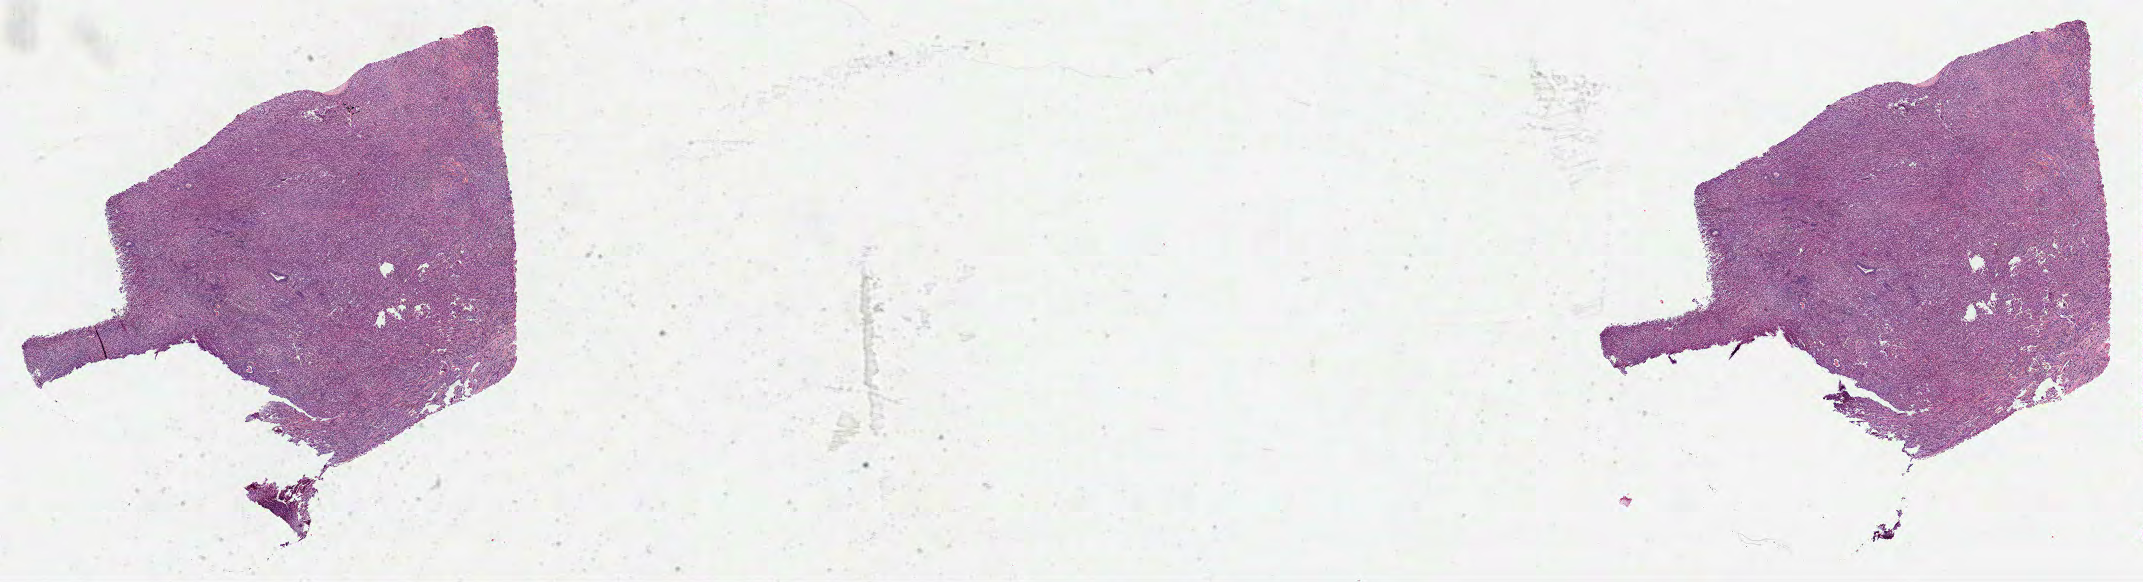
H&E whole-slide image, whole scanned area (about 34.6 x 9.4 mm, acquisition: 40x scan) shown as a low-resolution overview, formalin-fixed paraffin-embedded (FFPE) diagnostic section, sample: primary tumour, lung. Female patient; age at initial diagnosis 50 years.
TNM: T2 N1 MX. Diagnosis: Adenocarcinoma, NOS. AJCC pathologic stage: IIB (6th edition).